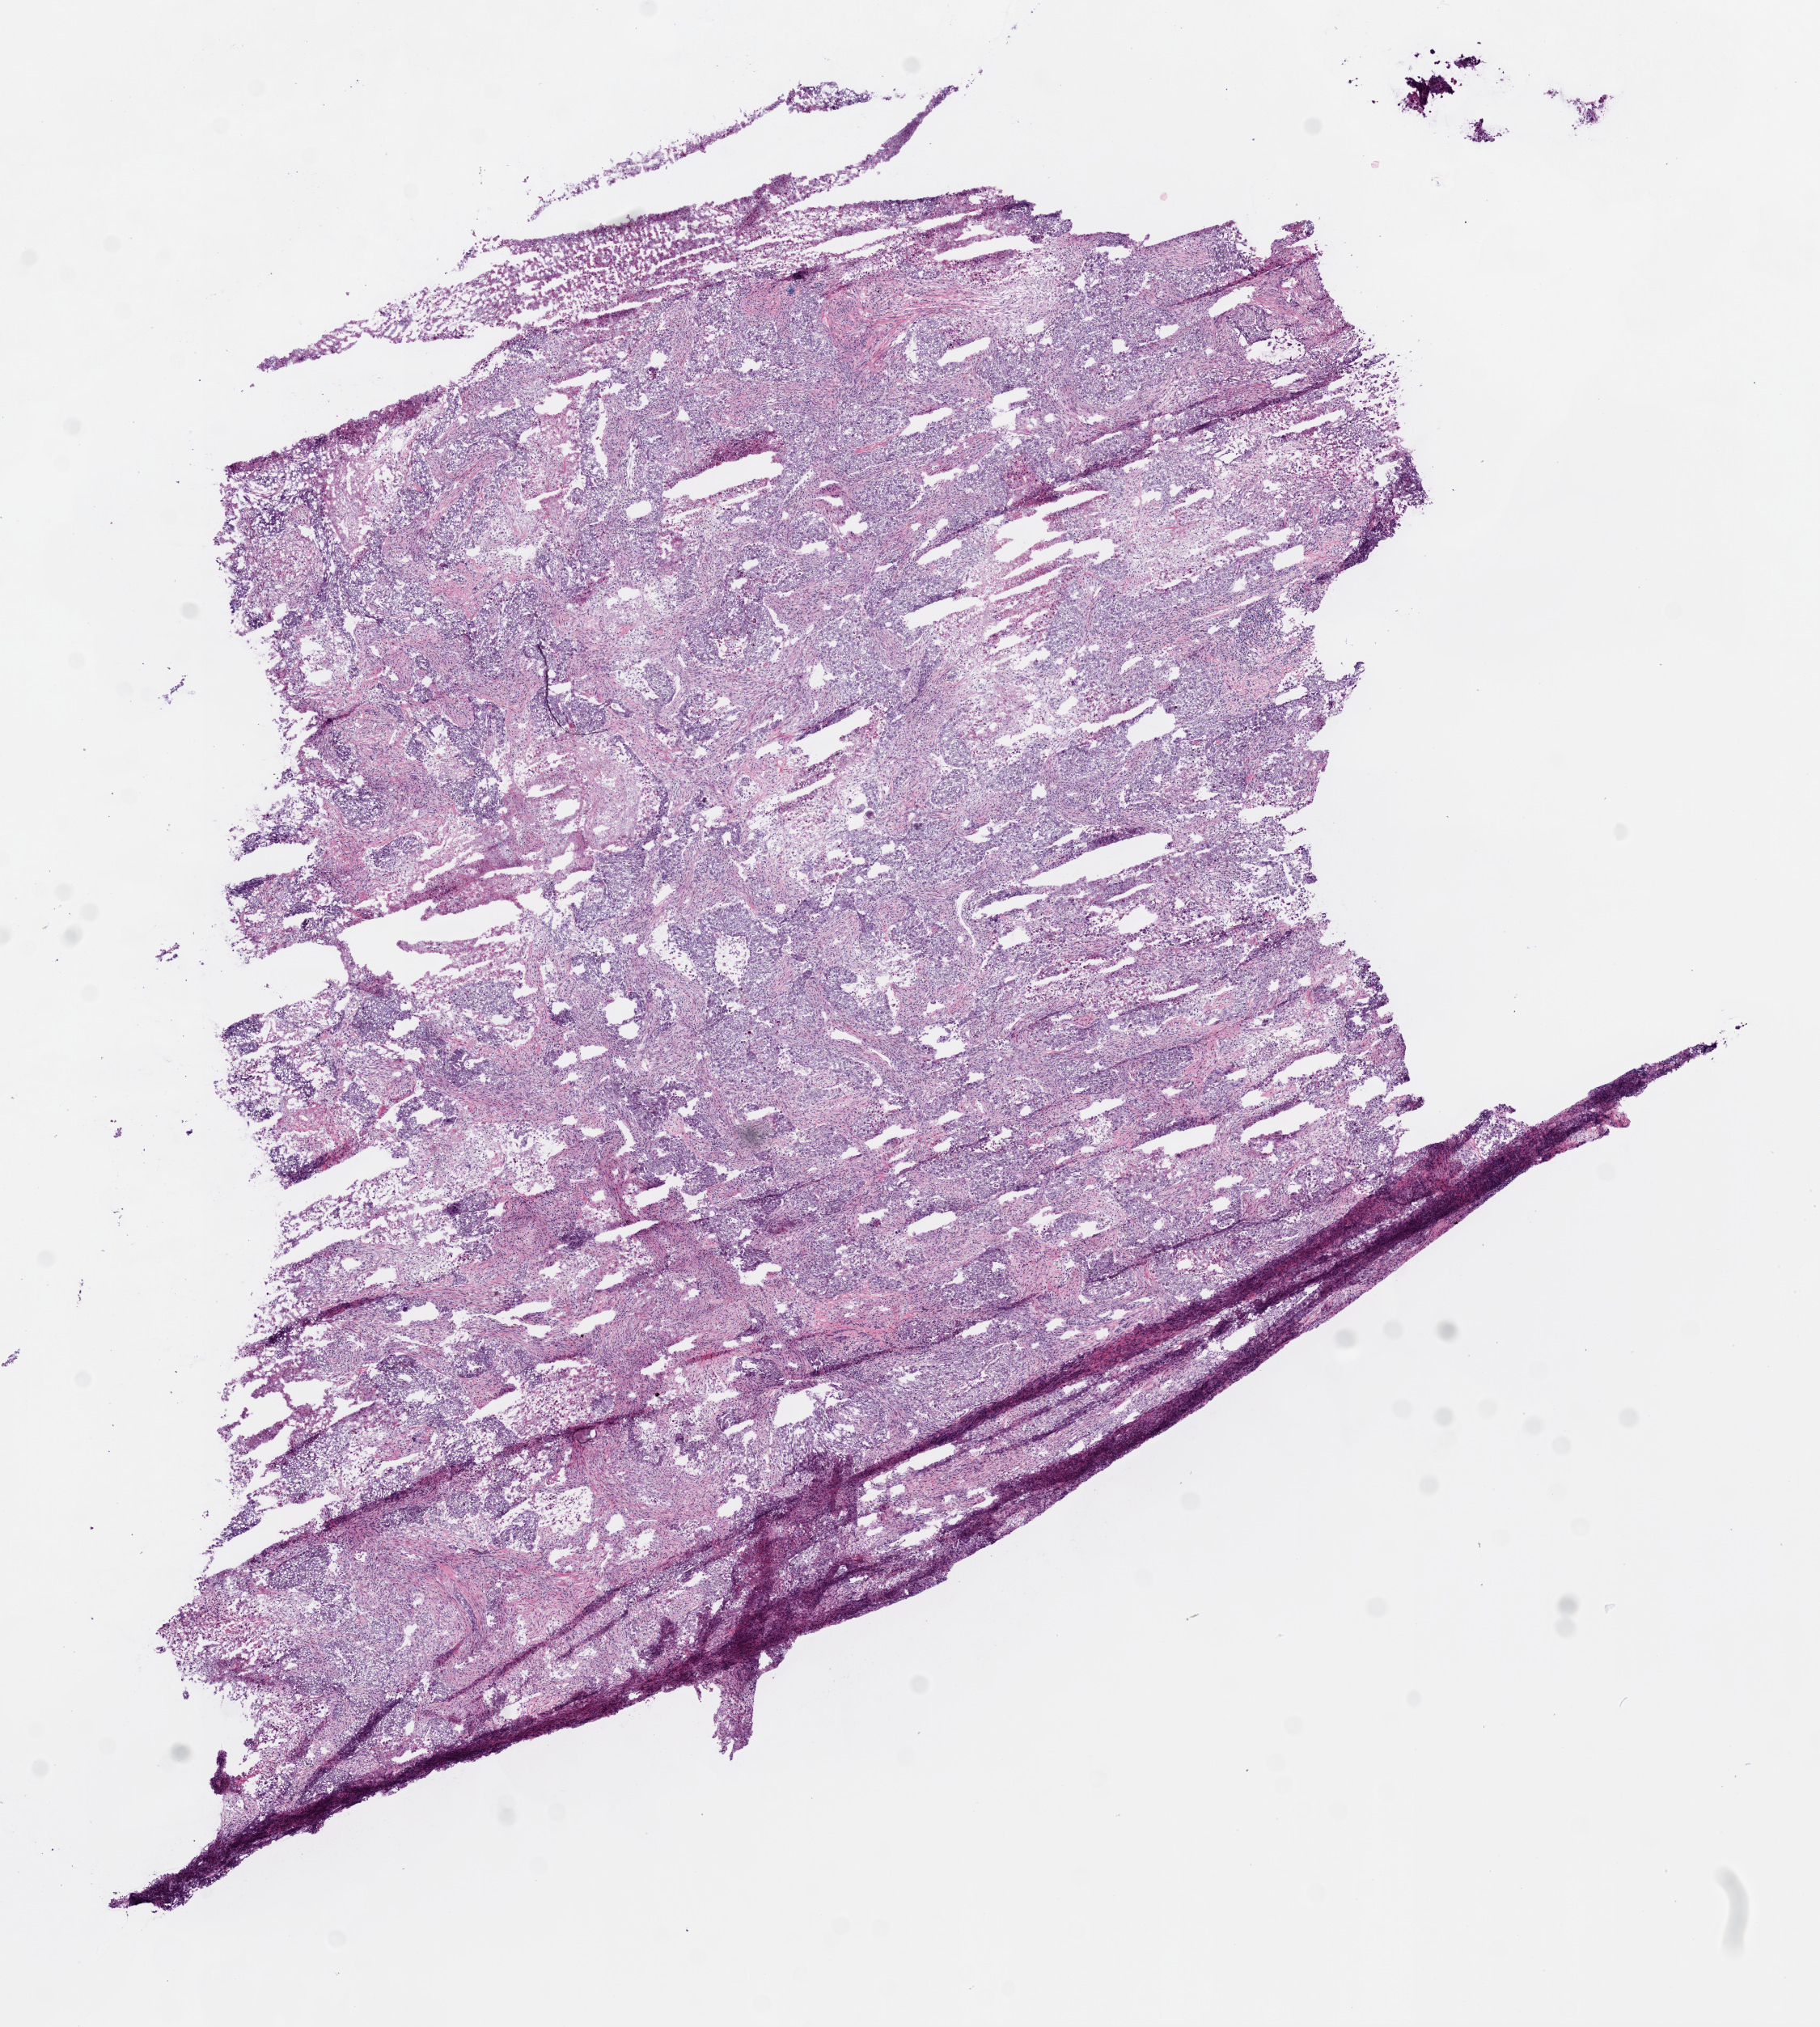
Whole-slide histology image, Hematoxylin and eosin (H&E) stained, whole scanned area (about 9.0 x 10.1 mm, acquisition: 20x scan) shown as a low-resolution overview, frozen section from the bottom of the tissue portion, lung, primary tumour sample. Male patient; age at initial diagnosis 65 years. Pathologist review of this section (percent, as recorded): tumour cells 77%, tumour nuclei 80%, normal cells 0%, stromal cells 13%, necrosis 10%. Inflammatory infiltration, as recorded: lymphocyte infiltration 5%.
• AJCC pathologic stage: IB (6th edition)
• histologic diagnosis: Adenocarcinoma, NOS